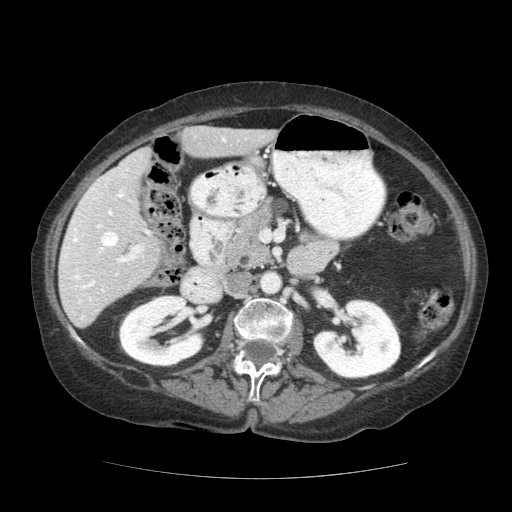
Contrast-enhanced abdominal CT (liver protocol), one axial slice; position 61 of 111 along the scan axis; reconstruction kernel STANDARD; soft-tissue window (W 400 / L 40 HU); 2.5 mm slice thickness; 512 × 512 image matrix, field of view 360 × 360 mm. Case-level facts recorded for this patient, not image findings: diagnosis: hepatocellular carcinoma (patient treated with transarterial chemoembolisation; whether this scan precedes or follows treatment is not stated here); TNM stage (as recorded): Stage-I; Child-Pugh class: A; tumour differentiation: moderately-poorly differentiated; tumour nodularity: uninodular.
Annotated regions visible in this slice (semi-automatically segmented with operator editing):
- liver parenchyma outside the tumour (the mass and vessels are separate outlines, so this box may not span the whole liver): bounding box <58,126,276,328> (left, top, right, bottom; pixels)
- liver vessels: <63,137,226,319>